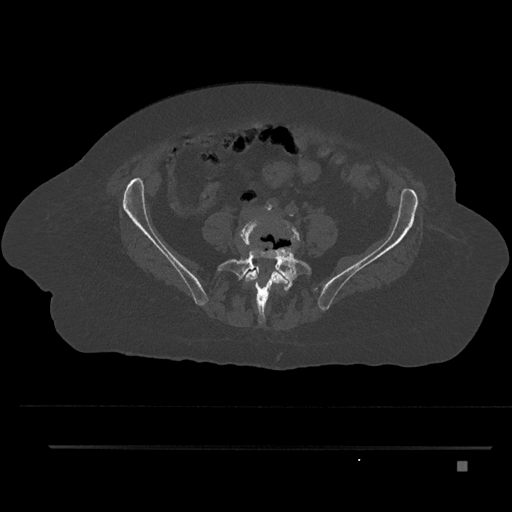
CT including the spine, one axial slice; position 52 of 797 along the scan axis; reconstruction kernel Br40s/3; bone window (W 1800 / L 400 HU); 0.5 mm slice thickness; 512 × 512 image matrix, field of view 437 × 437 mm. Patient: female, 76 years. Case-level facts recorded for this patient, not image findings: primary cancer: lung; vertebrae with lytic lesions (as recorded): T11, L3.
Annotated regions visible in this slice (semi-automatically segmented with operator editing):
- L4 vertebra: box from (x=238, y=217) to (x=300, y=307) px
- L5 vertebra: (x=217, y=248)–(x=312, y=324)